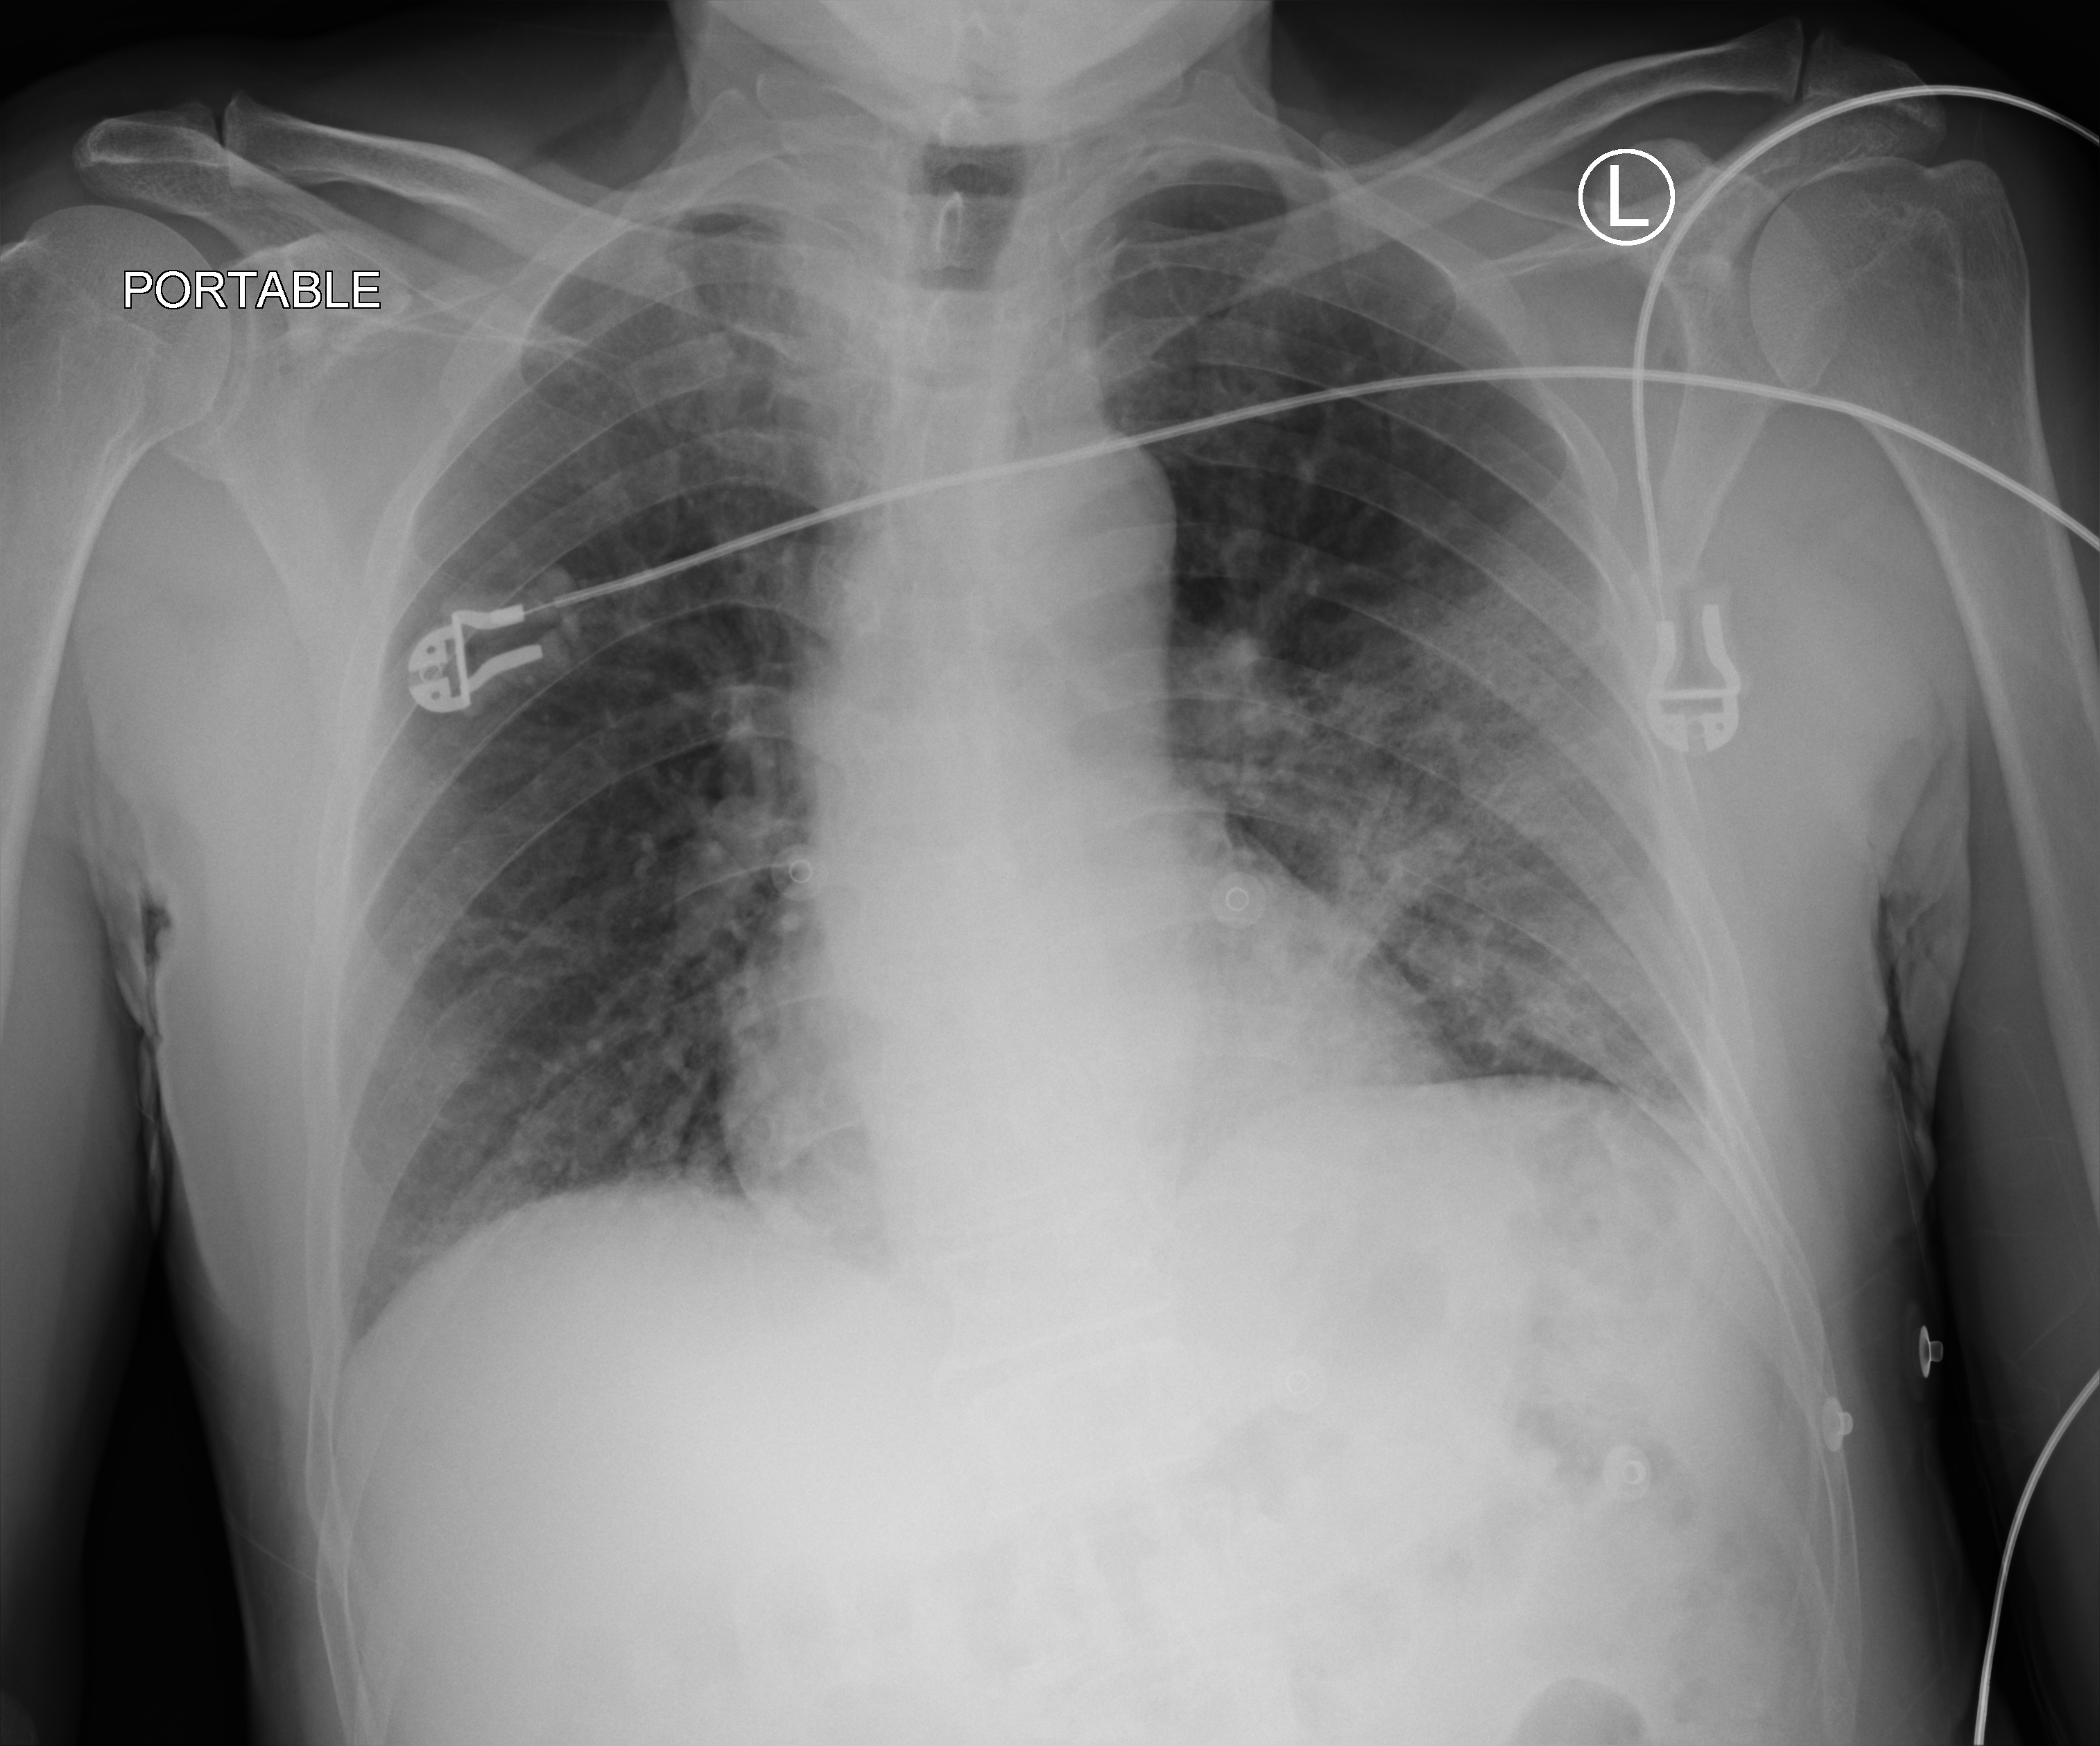
Portable chest radiograph, anteroposterior (AP) projection. Male patient hospitalised with COVID-19, age 60–74 years.
Hospital-stay facts (about this admission, not read from this image; timing relative to this image not recorded):
- mechanically ventilated during this hospital stay: no